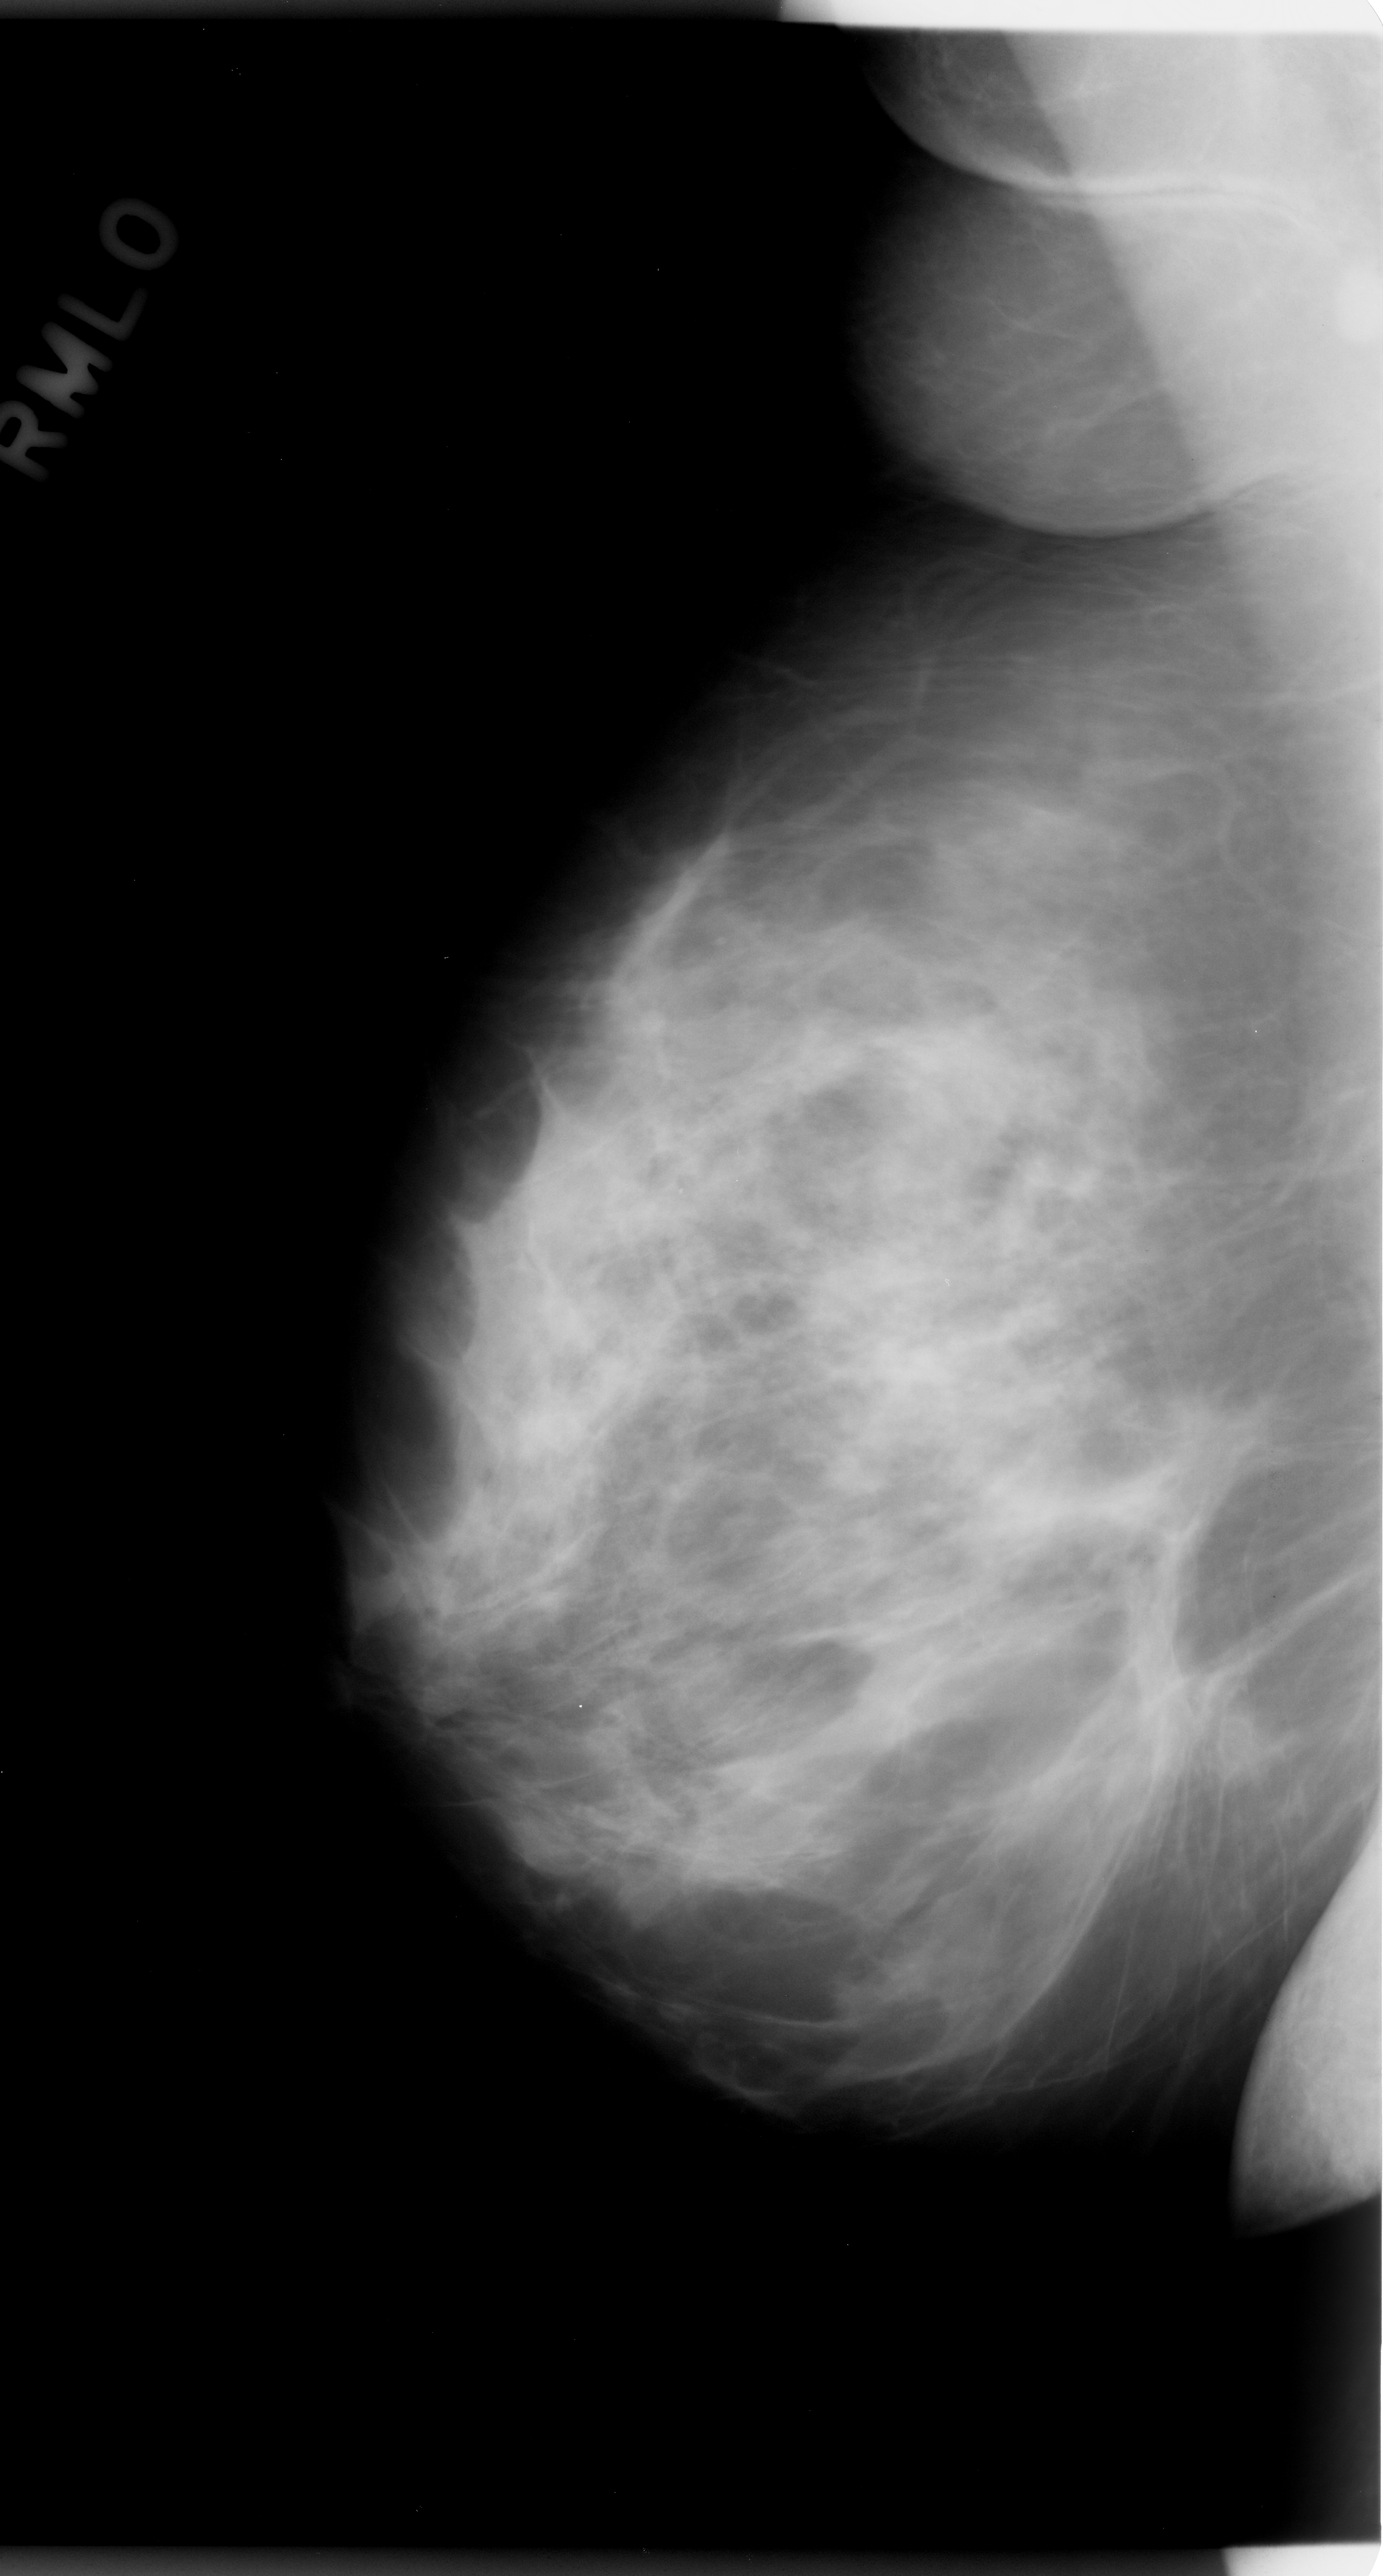
Digitized screen-film mammogram; right breast; mediolateral oblique (MLO) view; BI-RADS breast density category 3 (scale 1–4); 1383 × 2576 image matrix.
Marked abnormalities (boxes around the expert regions of interest):
- mass, shape architectural distortion, margins ill defined; BI-RADS assessment category 5; subtlety rating 5 on a 1 (subtle) to 5 (obvious) scale; pathology result (as recorded, not read from the image): malignant: bounding box (x1, y1, x2, y2) in pixels: (999, 1375, 1242, 1652)